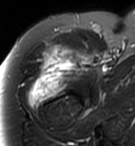
MRI of an extremity soft-tissue mass, one axial slice. Position 79 of 95 along the scan axis. T2-weighted fat-saturated. MR volume resampled by the dataset authors to the PET/CT grid (not the native acquisition matrix). 135 × 146 image matrix, field of view 132 × 143 mm. Female patient. From the clinical record (not read from this slice): histological type: pleiomorphic undifferentiated sarcoma; grade: high; site of the primary tumour: right quadricep.
Structures marked on this image (expert contour drawn on MRI and transferred to this co-registered scan by the dataset authors):
- gross tumour volume including surrounding oedema: bounding box <26,40,93,110> (left, top, right, bottom; pixels)
- gross tumour volume (mass): <41,40,93,85>